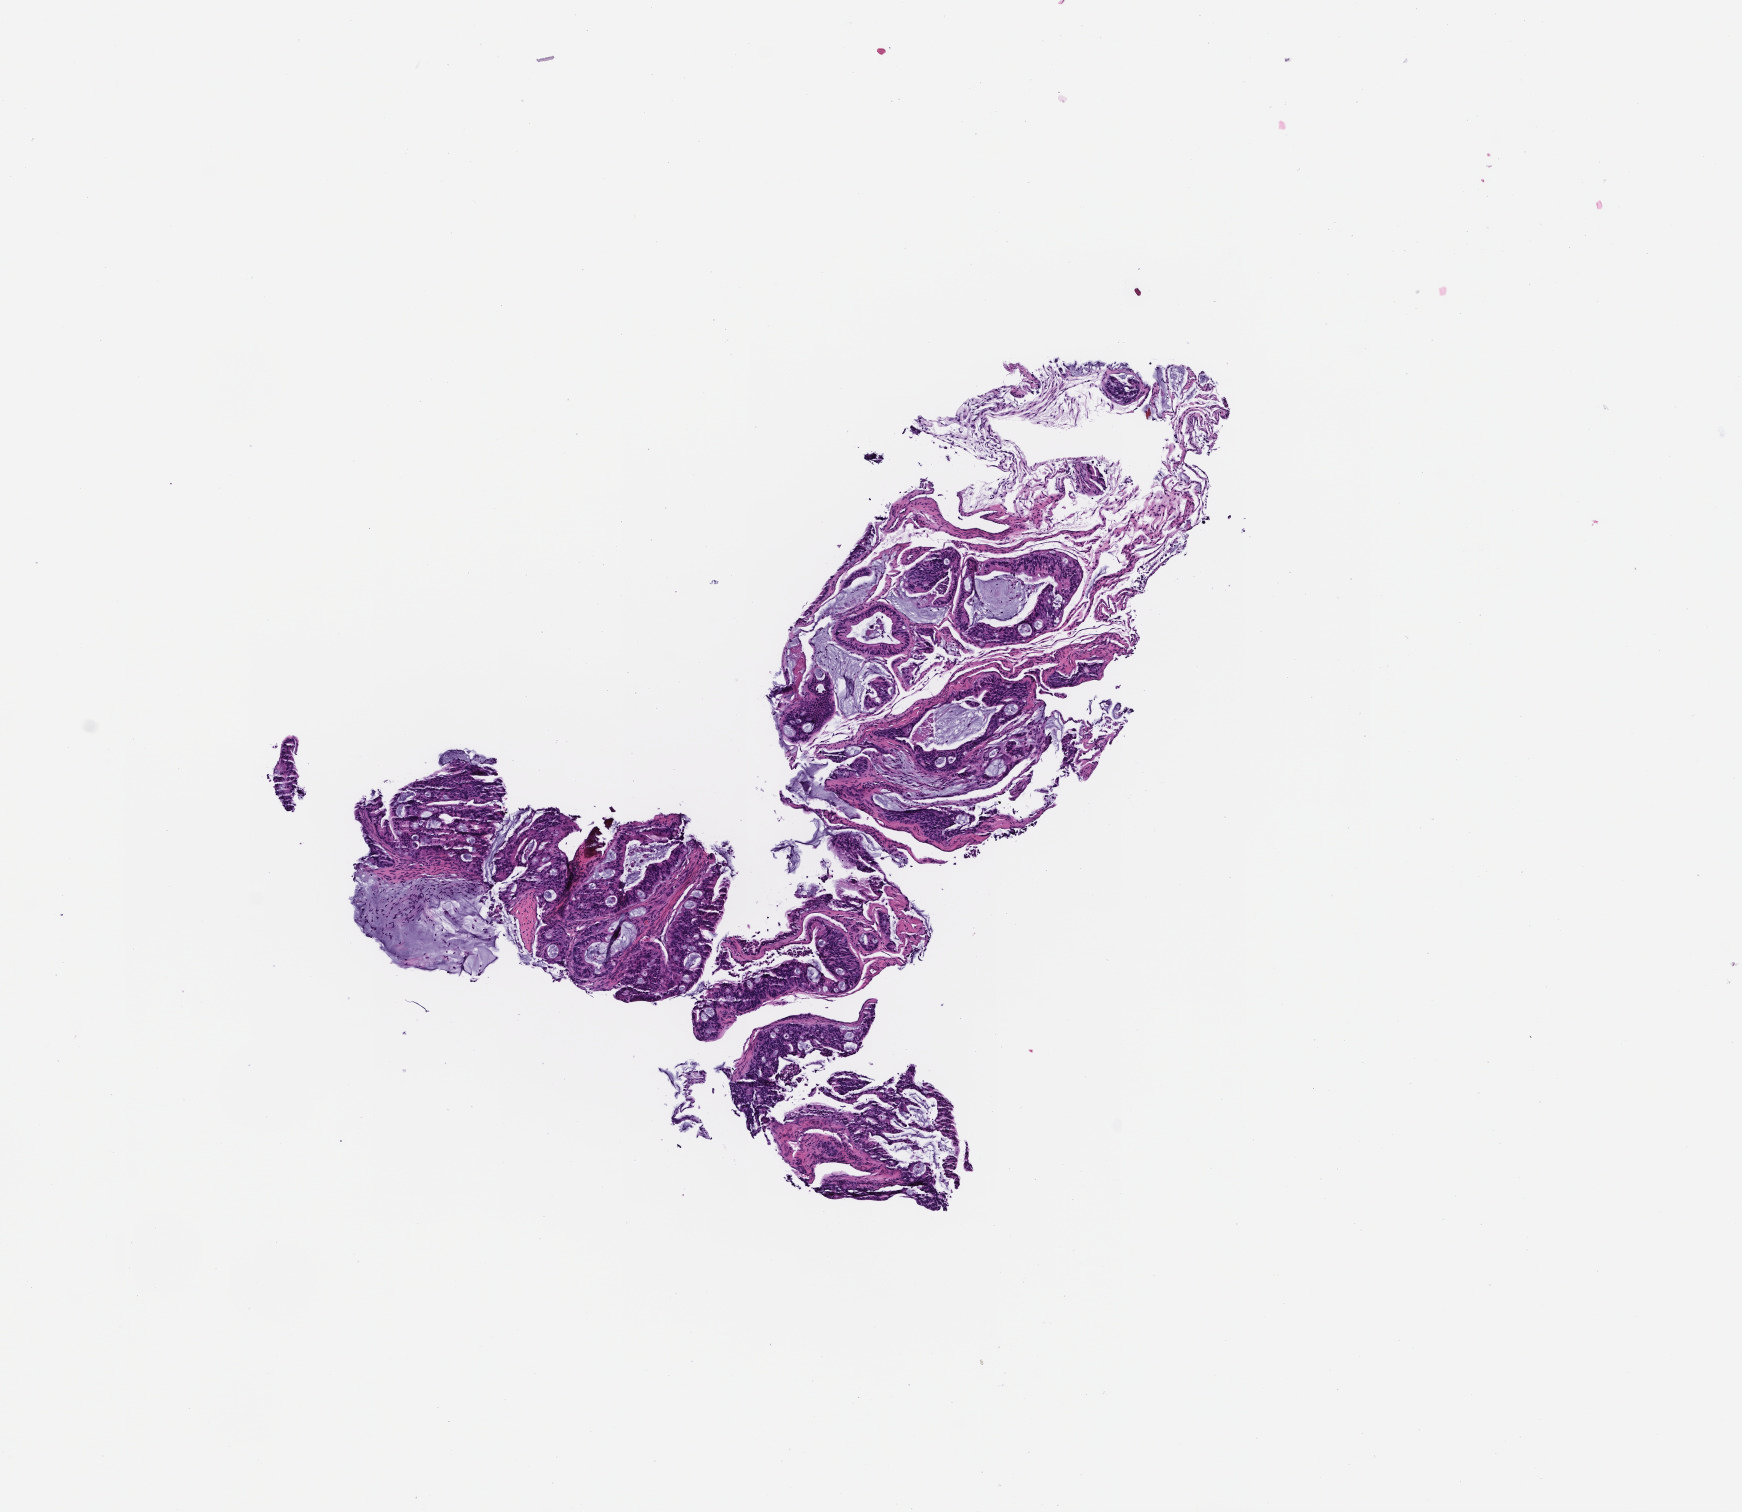
Hematoxylin and eosin (H&E) whole-slide image — whole scanned area (about 7.0 x 6.1 mm) shown as a low-resolution overview, FFPE section, specimen time point: collected at disease progression. Female patient.
• this section: metastatic tumor tissue
• primary diagnosis of the patient: Colorectal Carcinoma